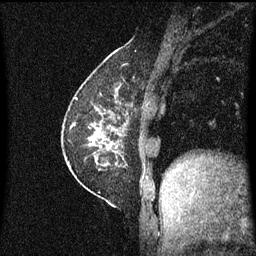
Breast MRI (dynamic contrast-enhanced), one sagittal slice; dynamic contrast-enhanced series, image 2 of 3 at this slice position (ordered by acquisition); 1.5 T; TE 4.2 ms, TR 8.4 ms; 2 mm slice thickness; 256 × 256 image matrix. Female patient, age 60 years.
Annotated regions visible in this slice (semi-automatically segmented with operator editing):
- analysis volume of interest (the breast-tissue region the enhancement analysis was run in; not a lesion): bounding box (x1, y1, x2, y2) in pixels: (69, 66, 134, 193)
- tumour enhancement mask (voxels above the 70 % enhancement threshold inside the analysis volume of interest): (92, 94, 128, 165)